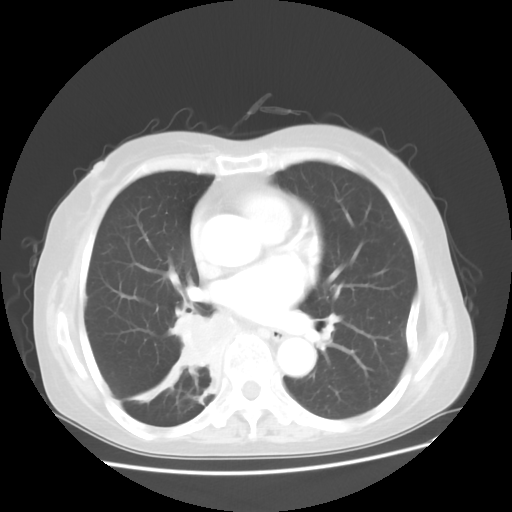
Chest CT, one axial slice; reconstruction kernel STANDARD; 120 kVp; lung window (W 1500 / L -600 HU); 5 mm slice thickness; 512 × 512 image matrix. Patient: female, 63 years. From the clinical record (not read from this slice): clinical TNM (as recorded): T2 N3 M1b.
Structures marked on this image (rectangle marked by the reading radiologist):
- lung tumour (recorded histology: small cell carcinoma): bounding box <172,306,224,372> (left, top, right, bottom; pixels)